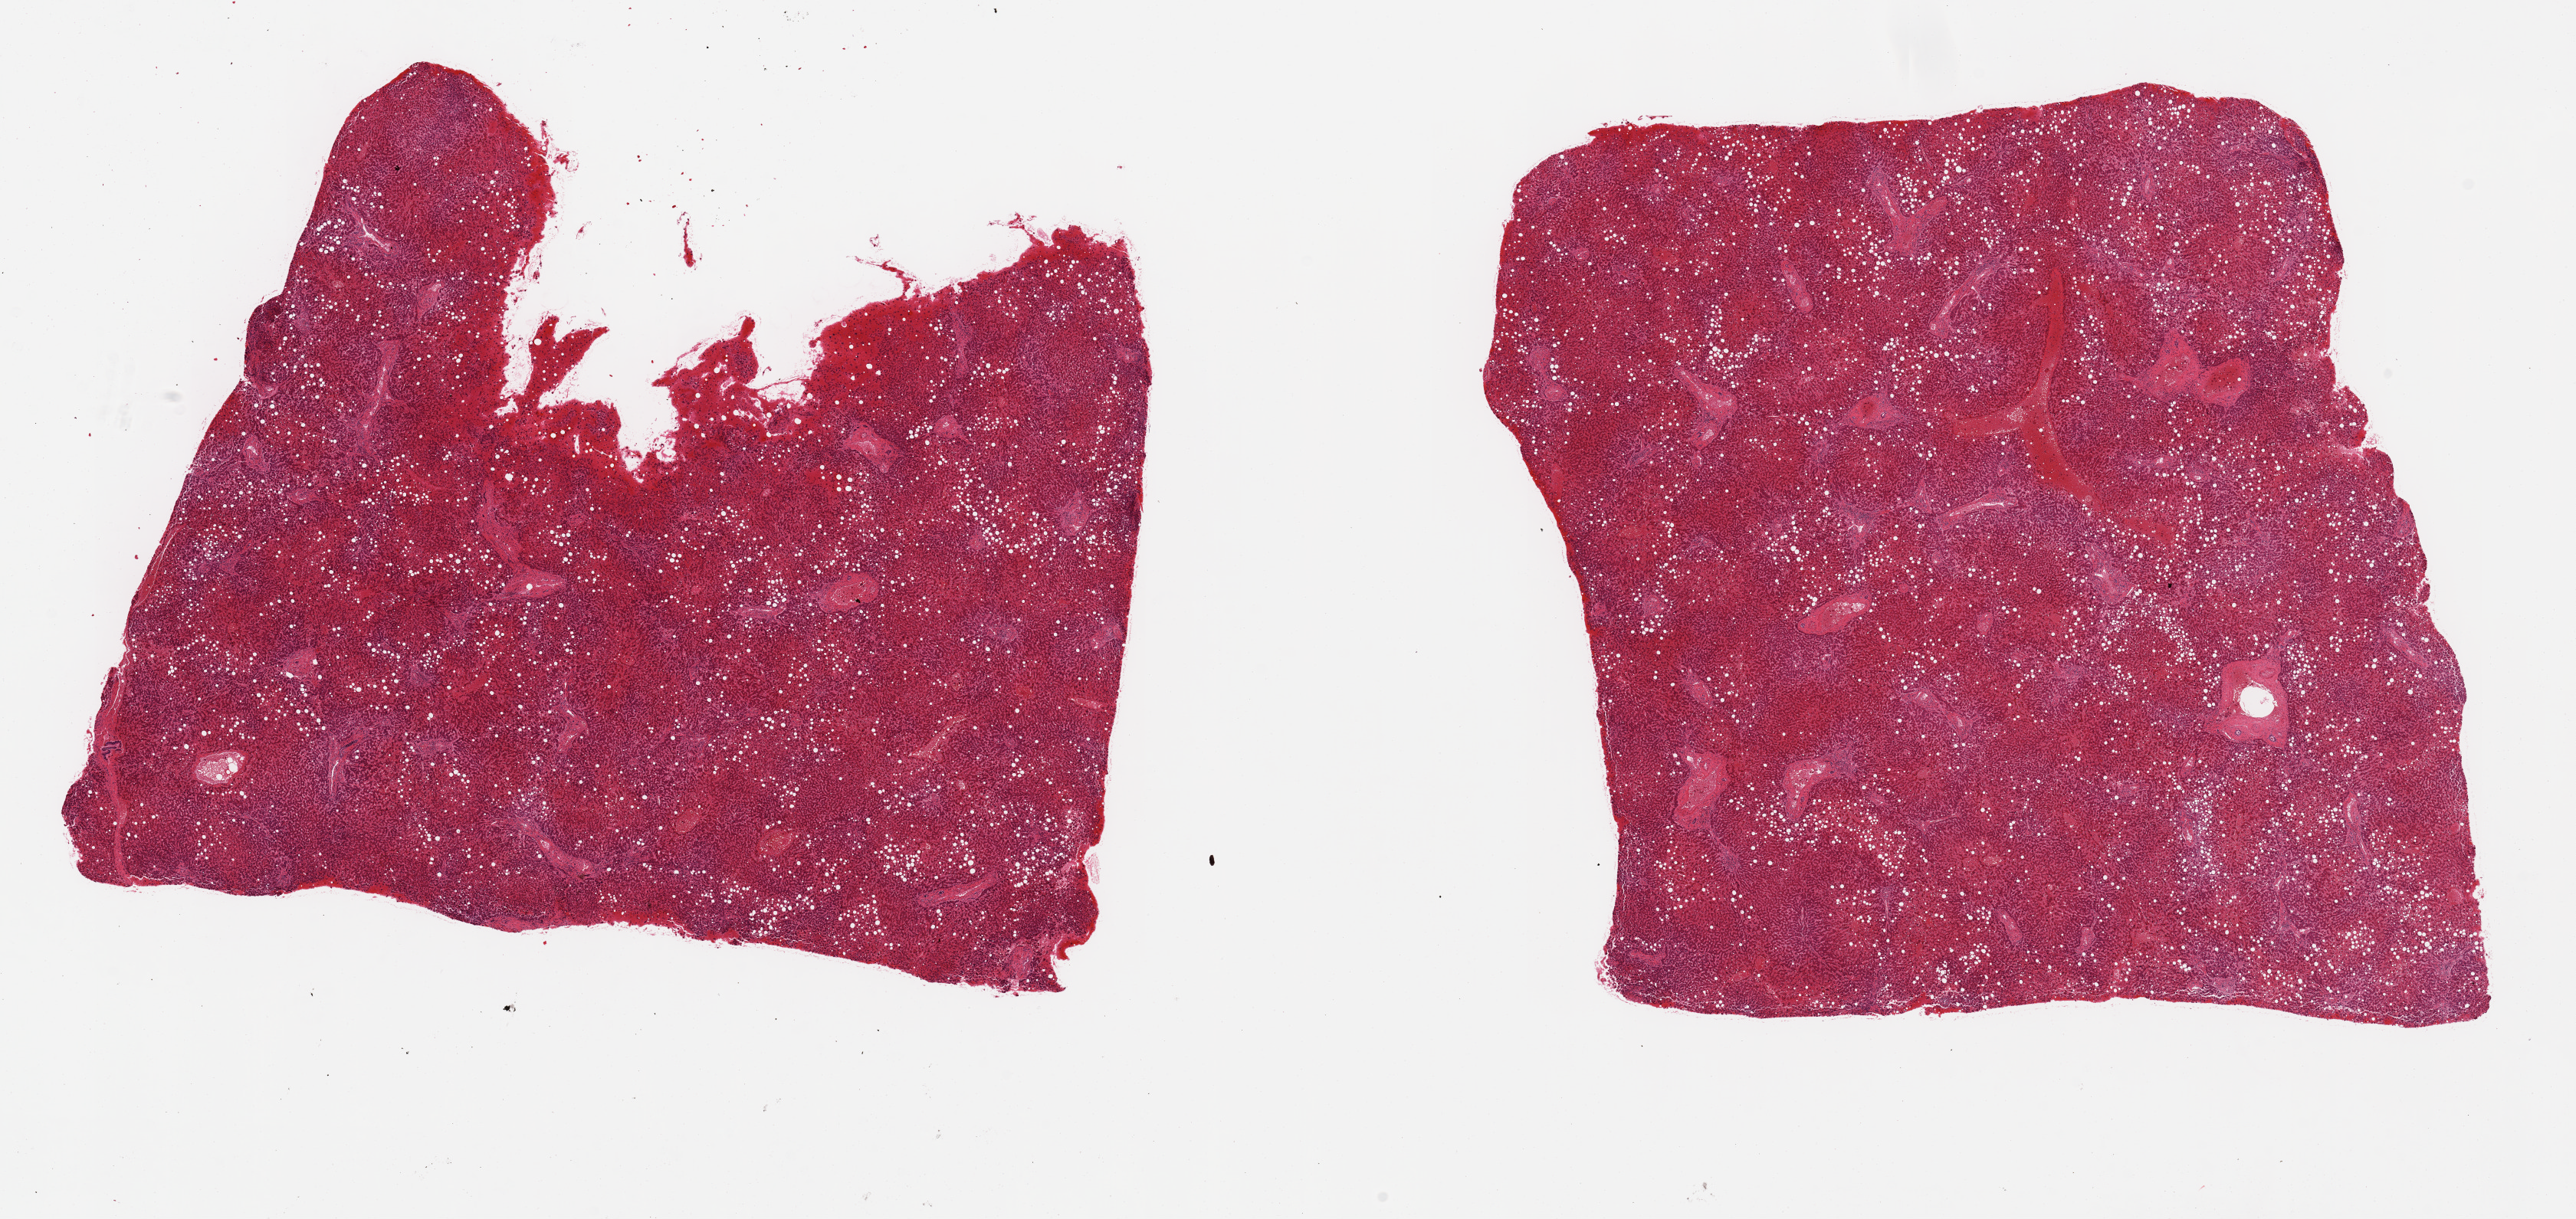
Hematoxylin and eosin (H&E) whole-slide image — low-resolution overview of the scanned area, about 26.6 x 12.6 mm (slide scanned at 20x). PAXgene-fixed, paraffin-embedded tissue. Section of liver (target tissue). Tissue donor sample. Male donor.
Pathologist's review note for this sample: 2 pieces, chronic steatohepatitis, macrovesicular steatosis is ~30% parenchyma; patchy early bridging fibrosis.